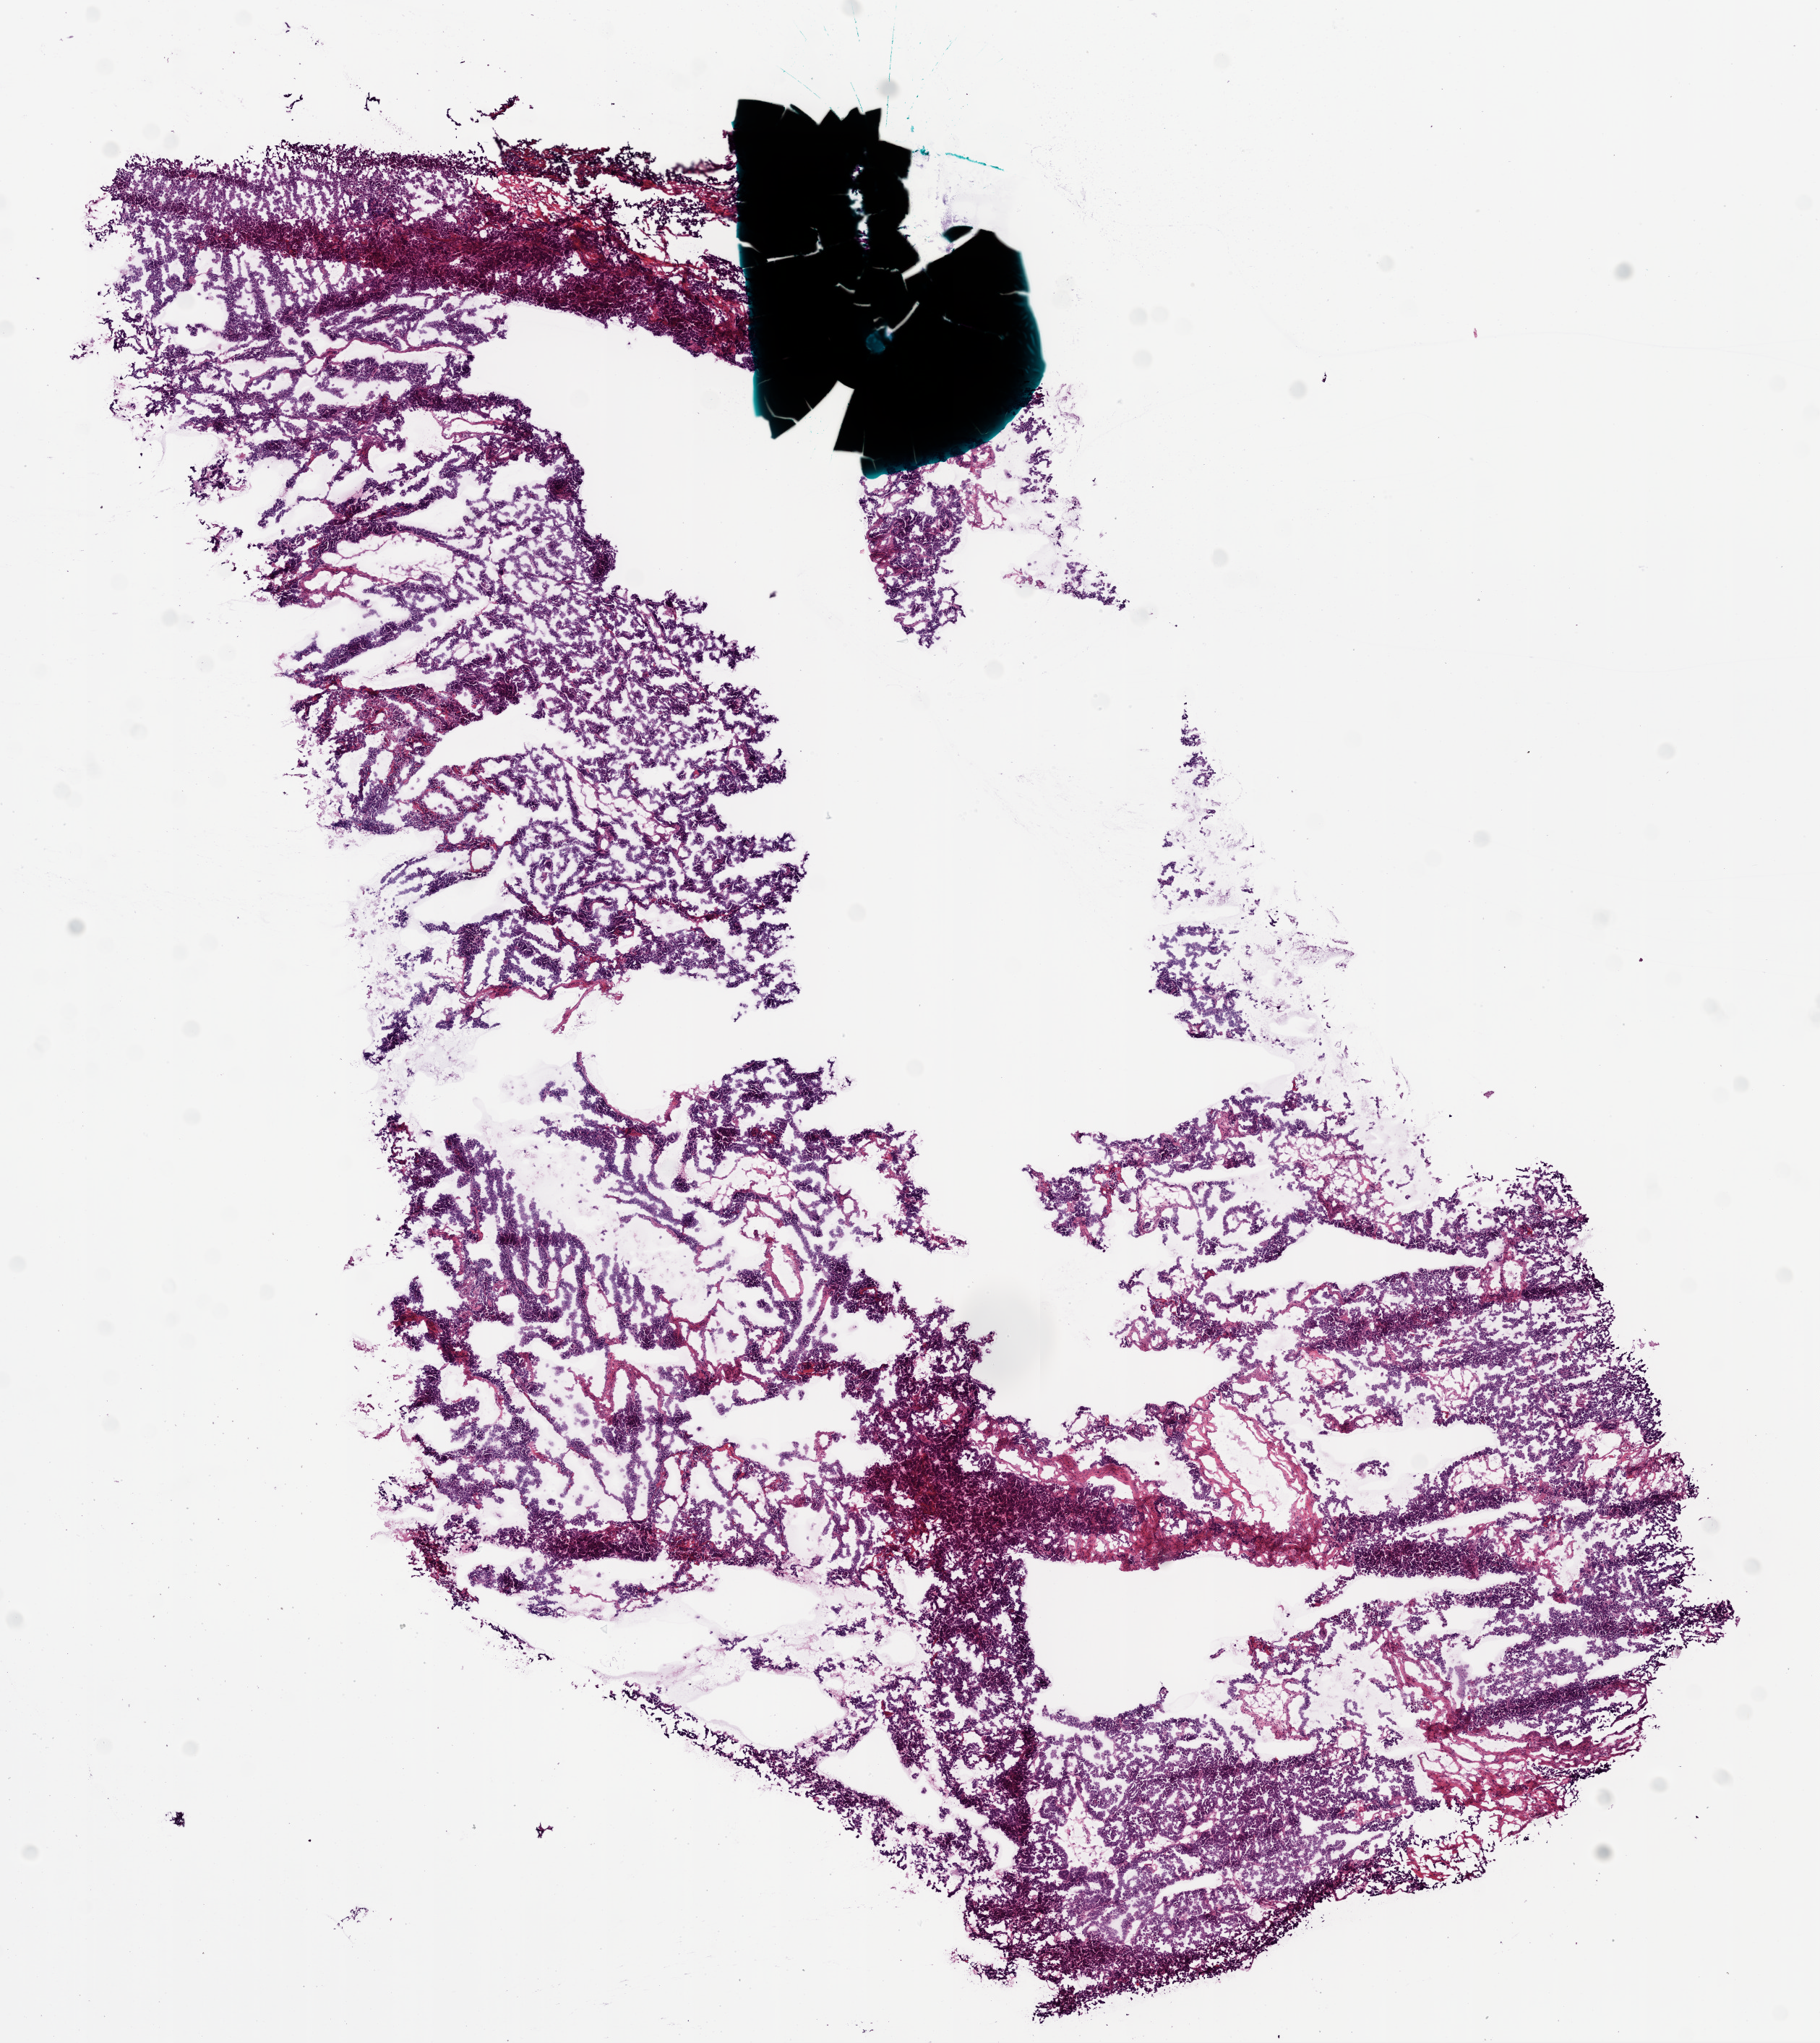
Whole-slide histology image, H&E-stained, low-resolution overview of the scanned area, about 10.2 x 11.4 mm; frozen section from the bottom of the tissue portion; sample: primary tumour, ovary. Female, age 61 years at initial diagnosis. Histologic grade: G3 (poorly differentiated). Pathologist review of this section (percent, as recorded): tumour cells 93%, tumour nuclei 99%, normal cells 0%, stromal cells 5%, necrosis 2%.
• FIGO stage: IIIC
• pathologic diagnosis: Serous cystadenocarcinoma, NOS